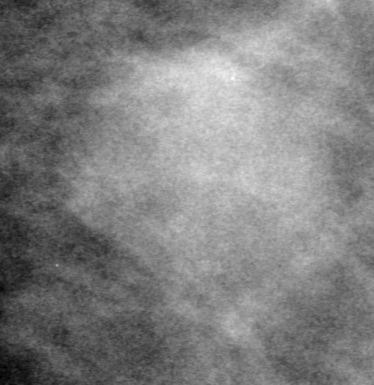
Crop from a digitized film mammogram around one marked abnormality, left breast, CC view, BI-RADS breast density category 2 (scale 1–4).
- Marked abnormality: mass, shape irregular, margins ill defined; BI-RADS assessment category 0 (incomplete: needs additional imaging); pathology (as recorded): benign.